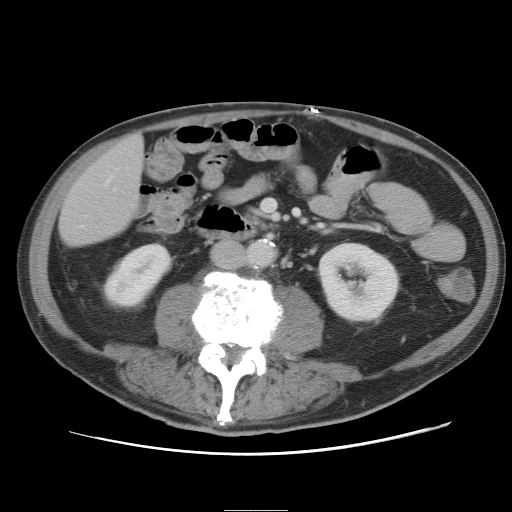
Contrast-enhanced abdominal CT, one axial slice; position 9 of 89 along the scan axis; 120 kVp; intravenous contrast given; soft-tissue window (W 400 / L 40 HU); 5 mm slice thickness; 512 × 512 image matrix, field of view 375 × 375 mm. Male patient, age 69 years. Case-level facts recorded for this patient, not image findings: diagnosis: colorectal cancer liver metastases, imaged before liver resection; multiple liver metastases: no; largest metastasis: 8.5 cm; disease in both lobes: no.
Outlined on this slice (expert manual segmentation):
- hepatic veins: bounding box (x1, y1, x2, y2) in pixels: (108, 179, 110, 182)
- liver: (60, 135, 144, 246)
- planned liver remnant (the part of the liver to remain after resection): (60, 135, 144, 246)